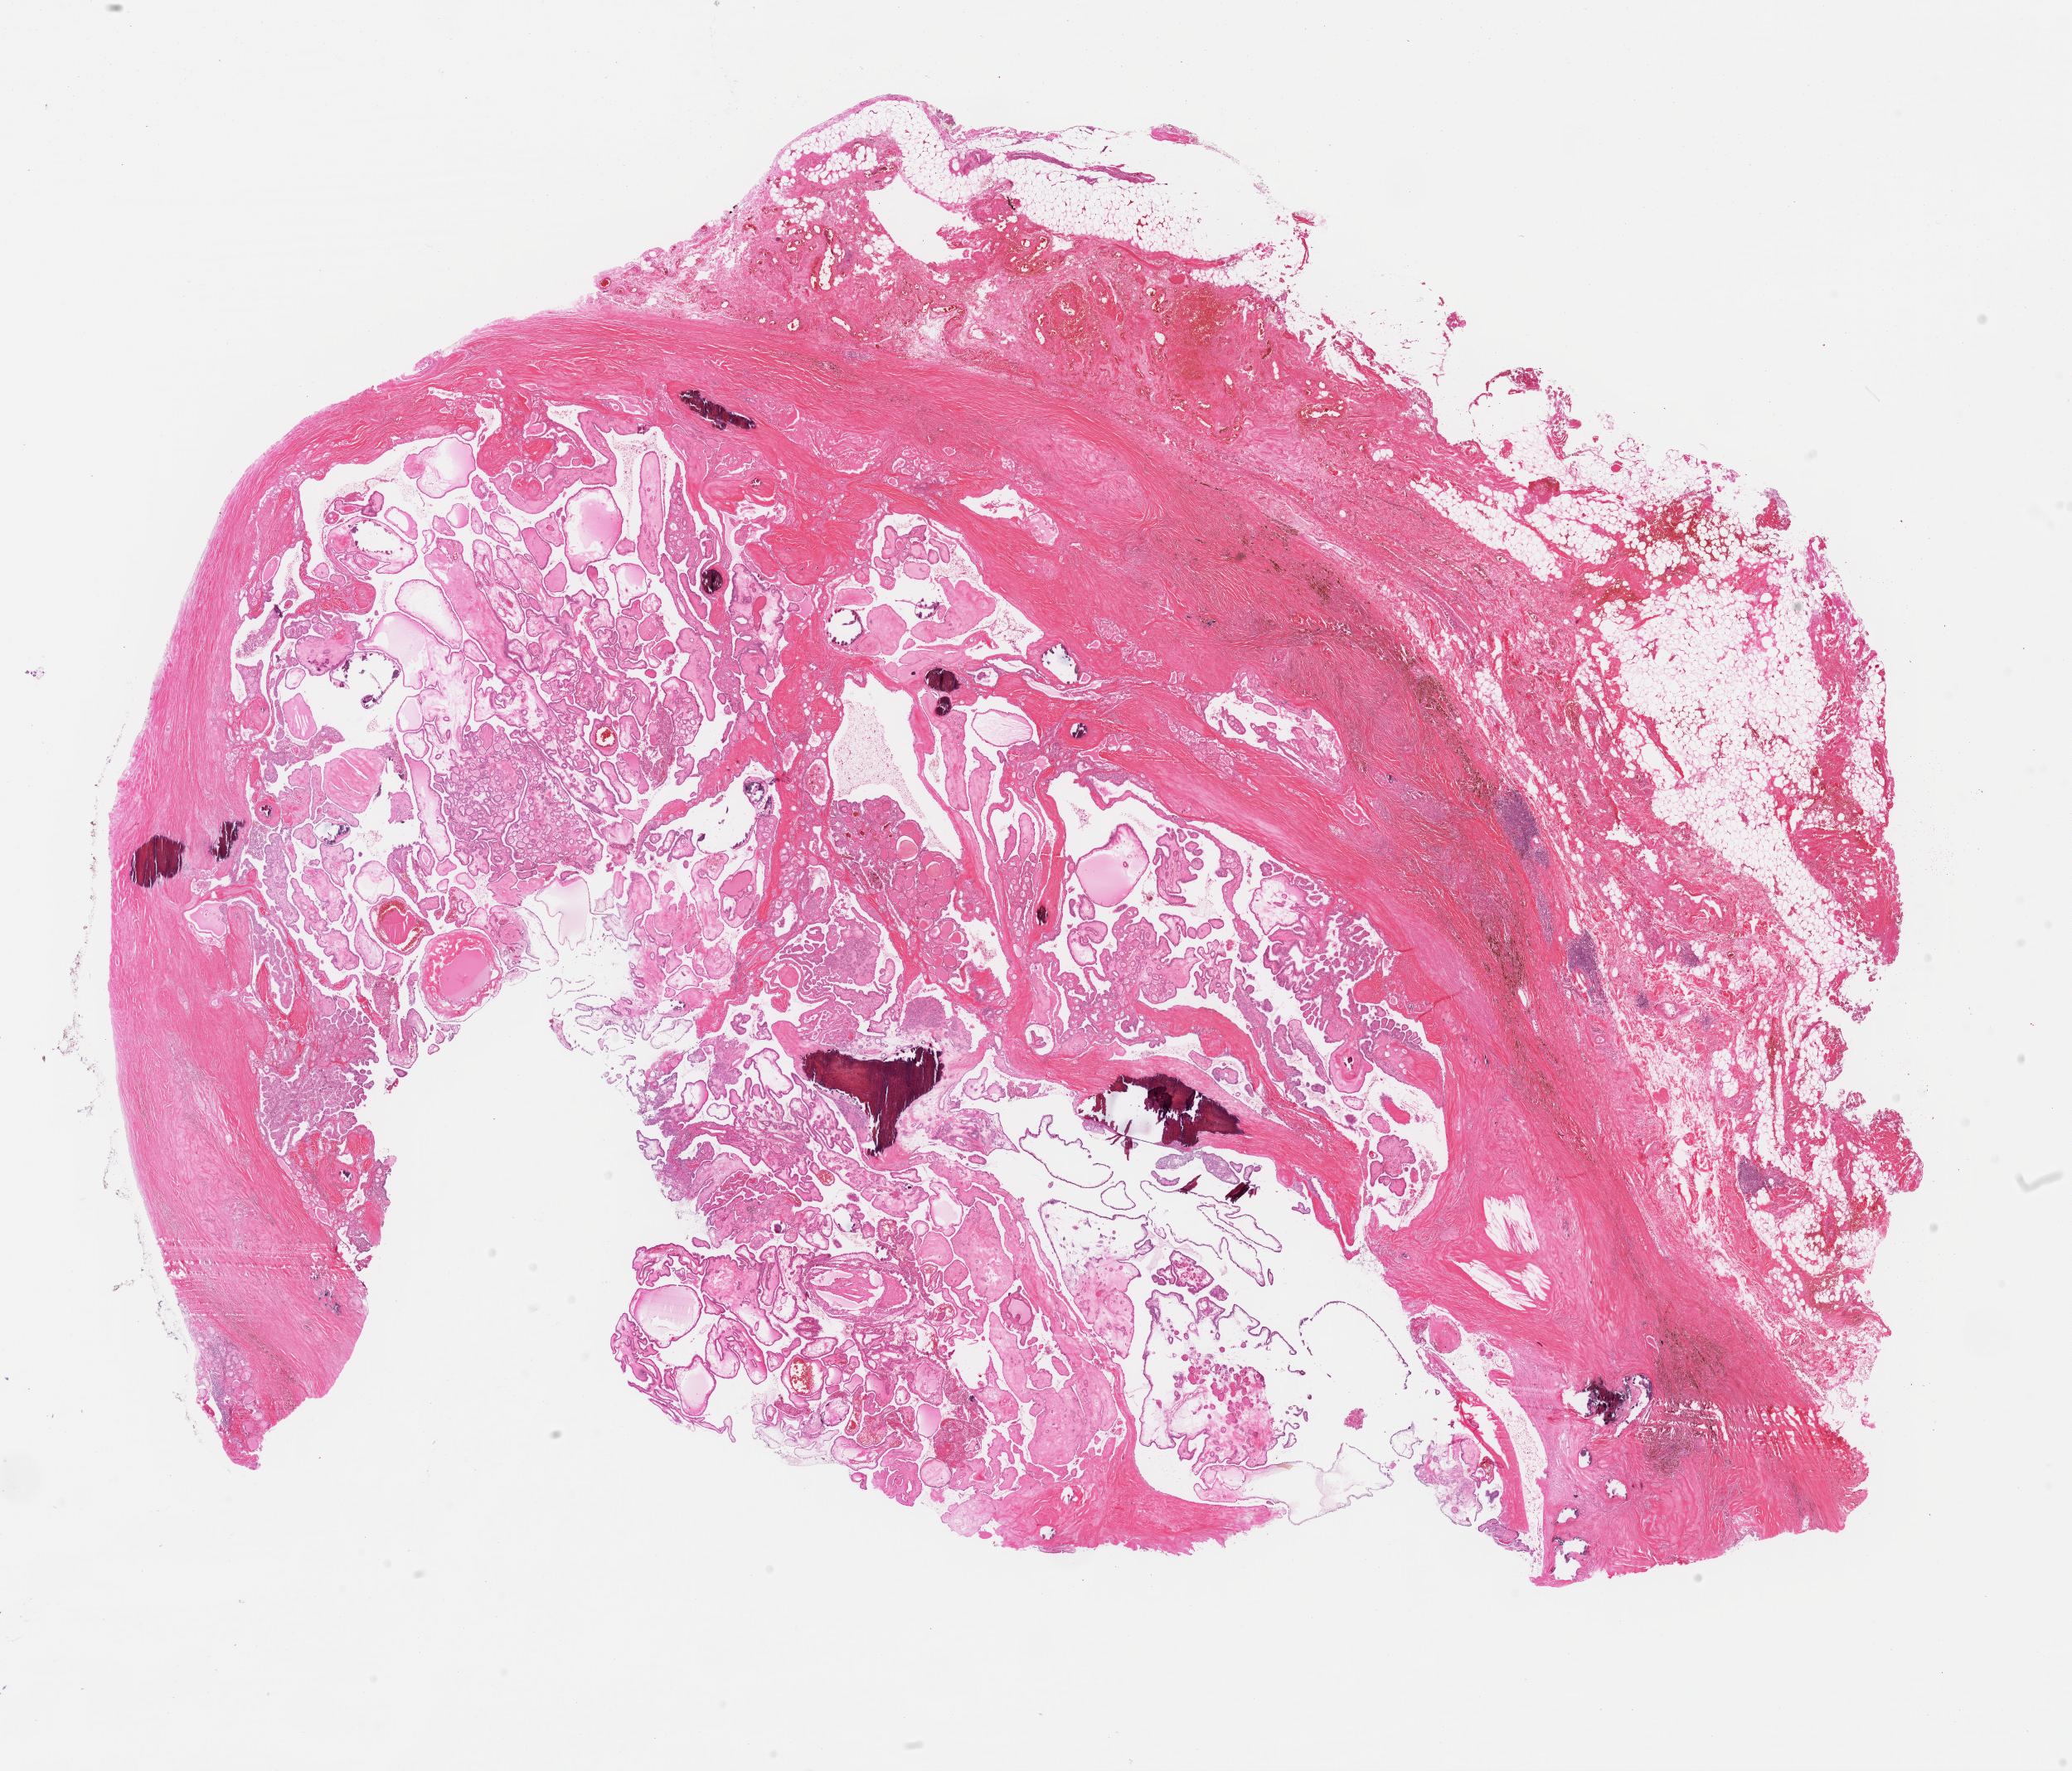
Whole-slide histology image, Hematoxylin and eosin (H&E) stained — whole scanned area (about 19.7 x 16.9 mm, from a 40x scan) shown as a low-resolution overview. Formalin-fixed paraffin-embedded (FFPE) diagnostic section. Sample: primary tumour, thyroid. Female patient; age at initial diagnosis 70 years.
Diagnosis: Papillary adenocarcinoma, NOS (thyroid gland).